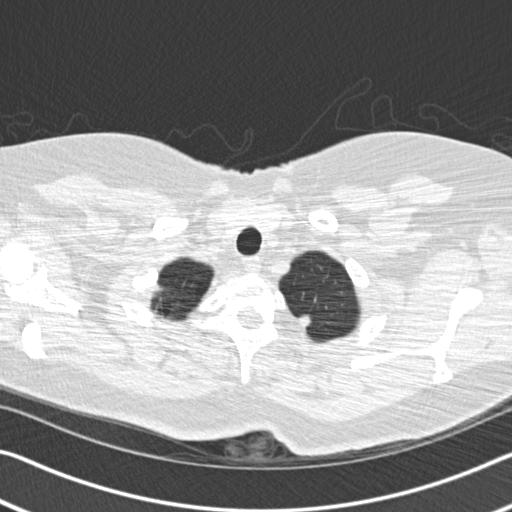
Axial slice from a low-dose chest CT screening exam. First (baseline) screen. Lung window (W 1500 / L -600 HU). 1.25 mm slice thickness. Standard (soft-tissue) reconstruction kernel (B30f). 120 kVp. Slice 26 of 233 in the series. 512 × 512 image matrix. Female participant, aged 60 years at enrolment. Former smoker at enrolment.
- Expert-annotated lung lesion, bounding box <280,305,324,344> (left, top, right, bottom; pixels).
- No non-calcified nodule or mass ≥4 mm was recorded by the screening reader at this exam.
- Official screen result: negative screen, minor abnormalities not suspicious for lung cancer.